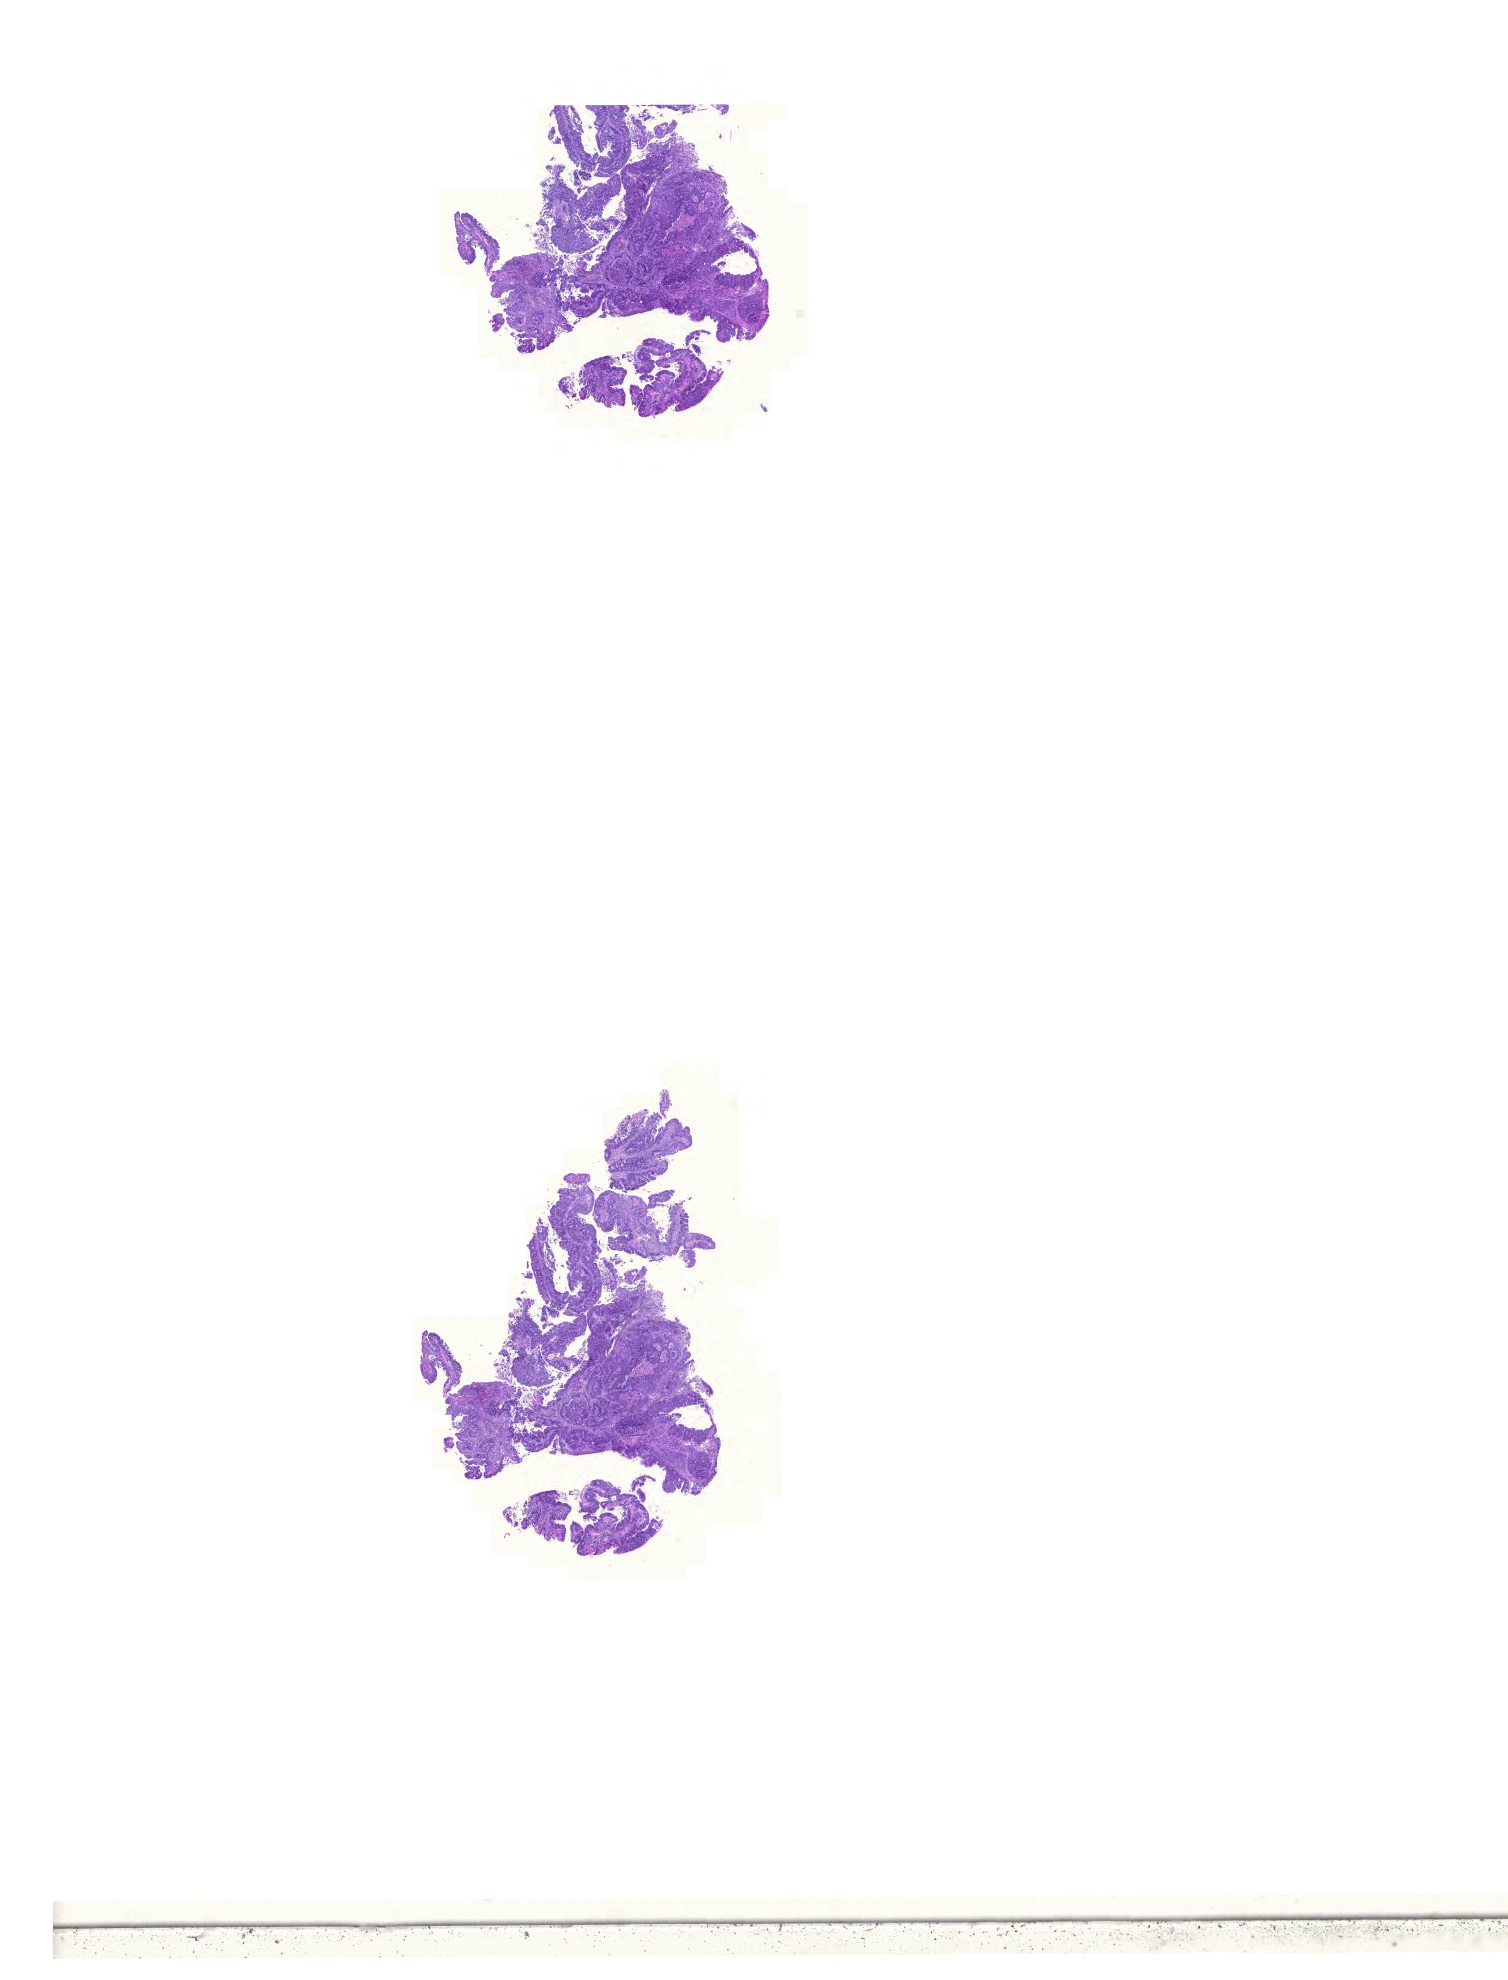
Whole-slide histology image, H&E — low-resolution overview of the scanned area, about 22.4 x 29.5 mm (slide scanned at 20x); formalin-fixed paraffin-embedded (FFPE) diagnostic section; colon, primary tumour sample. Female patient; age at initial diagnosis 61 years.
- TNM: T2 N0 M0
- AJCC pathologic stage: I
- diagnosis: Adenocarcinoma, NOS
- lymph nodes positive (case pathology): 0 of 21 examined